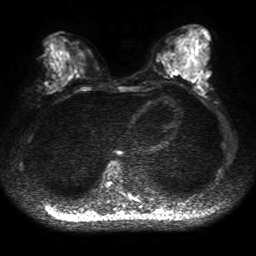
Breast MRI, one axial slice; slice 20 of 50 in the series (ordered by position); diffusion-weighted series; image 2 of 4 stored at this slice position (different b-values; order by instance number); 1.5 T; 256 × 256 image matrix, field of view 320 × 320 mm. Female patient.
Annotated regions visible in this slice (outlined manually by an expert reader):
- tumour on diffusion-weighted imaging: bounding box <45,82,58,94> (left, top, right, bottom; pixels)